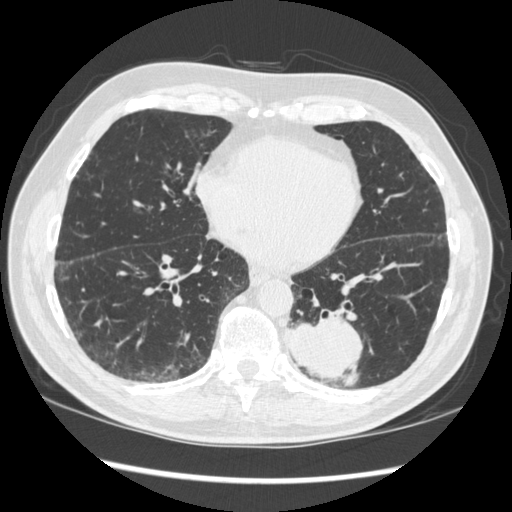
Low-dose screening chest CT, one axial slice. Slice 123 of 348 in the series (ordered by position). Reconstruction kernel STANDARD. Lung window (W 1500 / L -600 HU). 512 × 512 image matrix, field of view 360 × 360 mm.
Outlined on this slice (outlined manually by an expert reader):
- lesion 1 (tumor, lower lobe of left lung): bounding box [x1, y1, x2, y2] px = [287, 314, 362, 385]